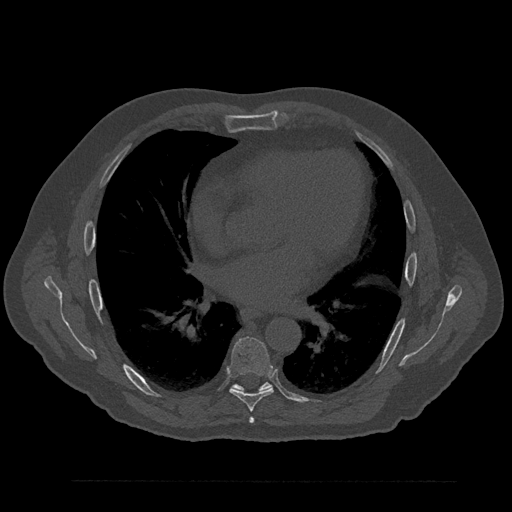
CT including the spine, one axial slice; position 493 of 797 along the scan axis; reconstruction kernel Br40s/3; bone window (W 1800 / L 400 HU); 0.5 mm slice thickness; 512 × 512 image matrix. Patient: male, 61 years. From the clinical record (not read from this slice): primary cancer: prostate.
Outlined on this slice (semi-automatic segmentation, software-assisted and operator-edited):
- T6 vertebra: box from (x=249, y=417) to (x=255, y=424) px
- T7 vertebra: (x=228, y=336)–(x=273, y=412)
- T8 vertebra: (x=232, y=382)–(x=272, y=392)